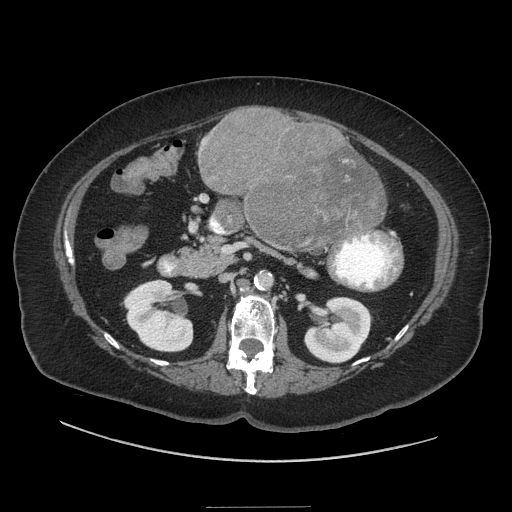
Contrast-enhanced abdominal CT (liver protocol), one axial slice. Position 2 of 81 along the scan axis. Reconstruction kernel STANDARD. Soft-tissue window (W 400 / L 40 HU). 2.5 mm slice thickness. 512 × 512 image matrix, field of view 440 × 440 mm. Case-level facts recorded for this patient, not image findings: diagnosis: hepatocellular carcinoma (patient treated with transarterial chemoembolisation; whether this scan precedes or follows treatment is not stated here); TNM stage (as recorded): Stage-II; Child-Pugh class: A; tumour differentiation: moderately differentiated; tumour nodularity: multinodular.
Annotated regions visible in this slice (semi-automatically segmented with operator editing):
- liver parenchyma outside the tumour (the mass and vessels are separate outlines, so this box may not span the whole liver): box from (x=198, y=107) to (x=386, y=236) px
- mass: (x=198, y=107)–(x=385, y=250)